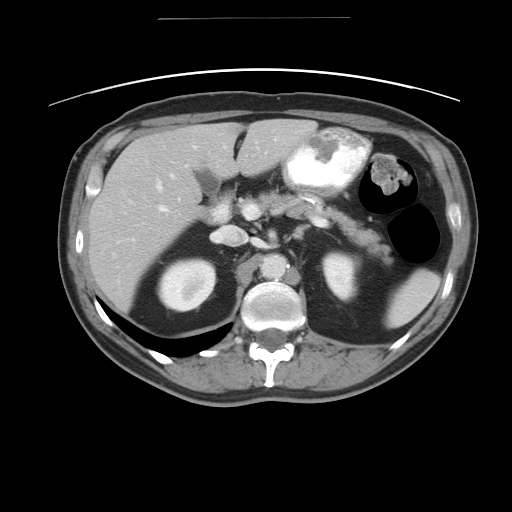
Contrast-enhanced abdominal CT, one axial slice. 120 kVp. Soft-tissue window (W 400 / L 40 HU). 5 mm slice thickness. 512 × 512 image matrix. Male patient, age 57 years. From the clinical record (not read from this slice): diagnosis: colorectal cancer liver metastases, imaged before liver resection; multiple liver metastases: yes; largest metastasis: 4 cm; disease in both lobes: no.
Outlined on this slice (manually delineated by an expert):
- hepatic veins: bounding box [x1, y1, x2, y2] px = [111, 145, 195, 256]
- liver: [89, 119, 316, 312]
- planned liver remnant (the part of the liver to remain after resection): [212, 119, 316, 177]
- portal vein (with intrahepatic branches): [116, 144, 225, 243]